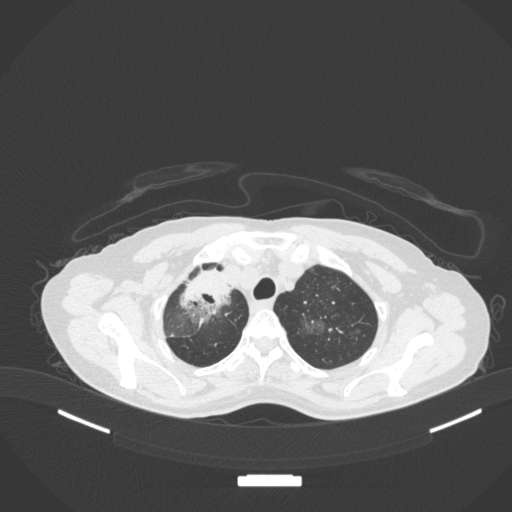
Chest CT, one axial slice; position 274 of 311 along the scan axis; reconstruction kernel B31f; lung window (W 1500 / L -600 HU); 512 × 512 image matrix. Patient: female, 59 years. Case-level facts recorded for this patient, not image findings: clinical TNM (as recorded): T3 N0 M0; histopathological grade: G1.
Structures marked on this image (bounding box drawn by a radiologist):
- lung tumour (recorded histology: adenocarcinoma): bounding box <174,261,230,326> (left, top, right, bottom; pixels)